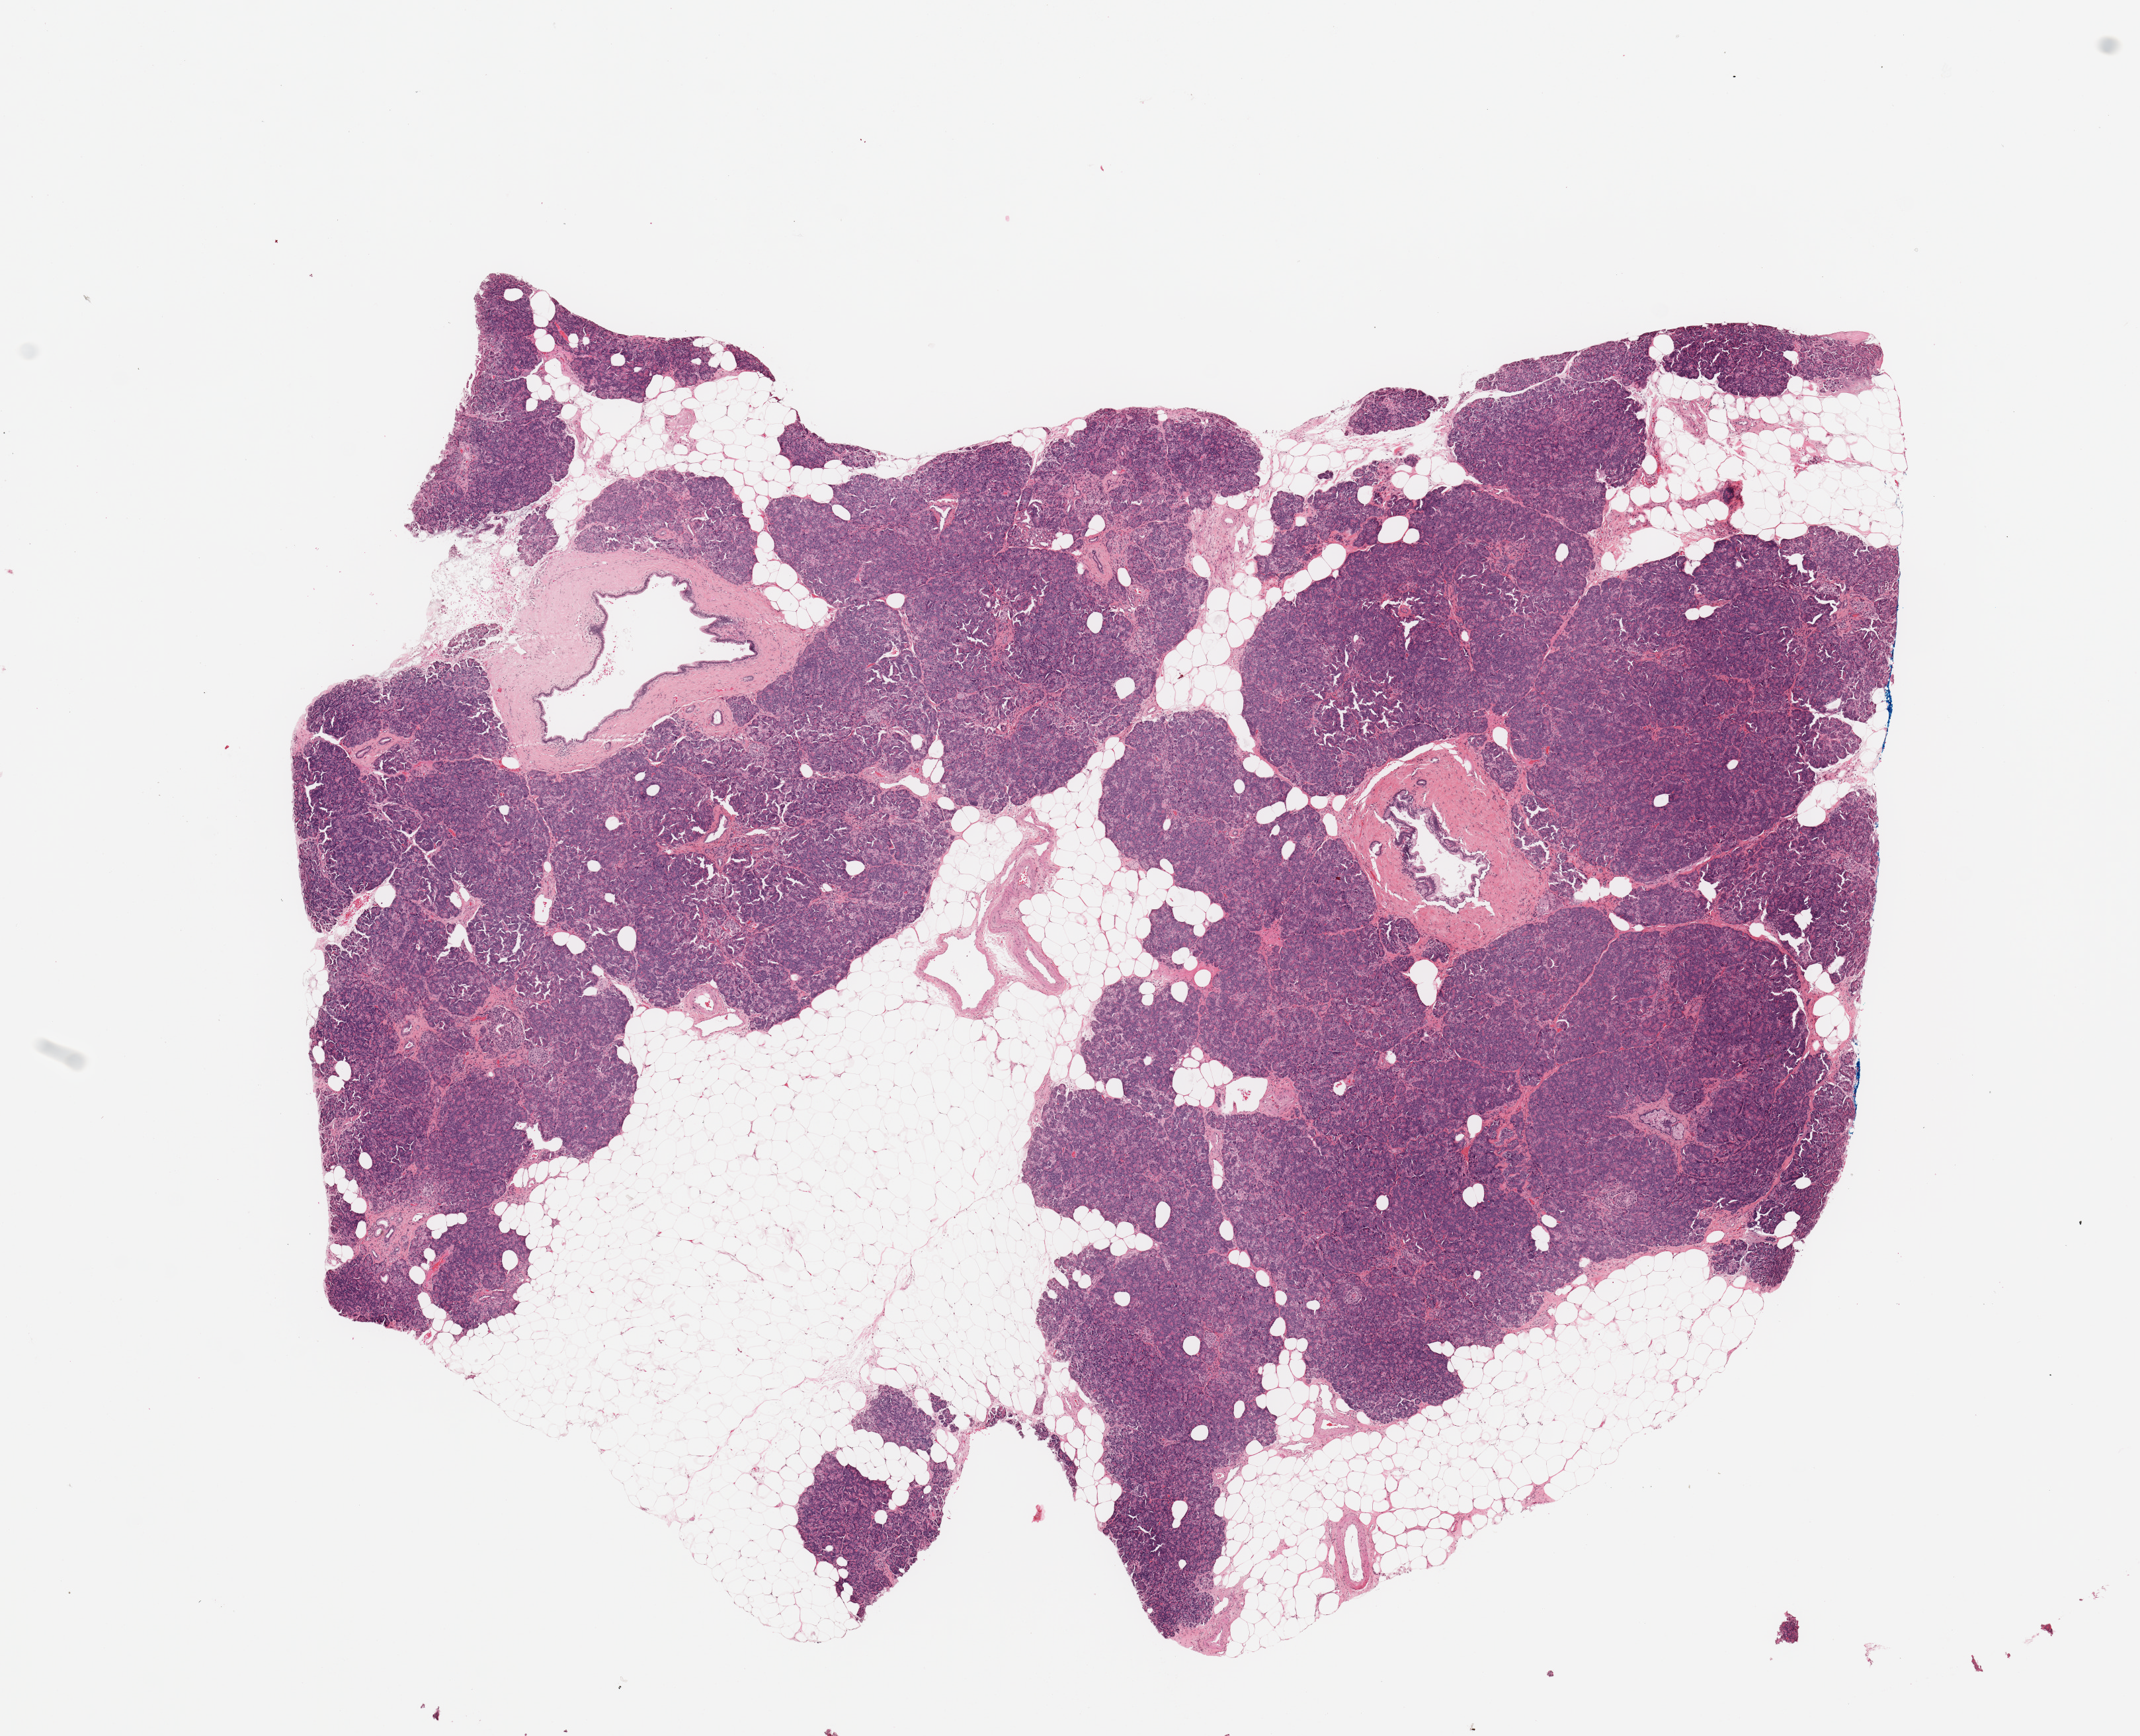
Digitized H&E-stained tissue section (whole slide) — whole scanned area (about 12.8 x 10.4 mm) shown as a low-resolution overview; normal (non-tumour) tissue sample, sampled site: pancreas. Patient: female, age 70 years.
This section: normal (non-tumour) tissue from the same patient. Patient diagnosis: Infiltrating duct carcinoma, NOS.